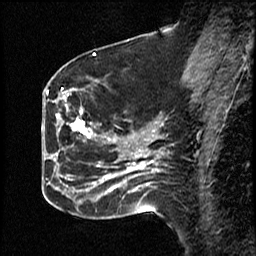
Breast MRI (dynamic contrast-enhanced), one sagittal slice; slice 23 of 50 in the series (ordered by position); dynamic contrast-enhanced study with each time point stored as its own series, time point 2 of 4 at this slice position (early post-contrast, ordered by acquisition time); 1.5 T; TE 4.2 ms, TR 18.5 ms; 256 × 256 image matrix, field of view 200 × 200 mm. Patient: female, 44 years. Case-level facts recorded for this patient, not image findings: setting: breast cancer imaged before/during neoadjuvant chemotherapy; receptor status: HR-positive, HER2-negative.
Annotated regions visible in this slice (semi-automatic segmentation, software-assisted and operator-edited):
- analysis volume of interest (the breast-tissue region the enhancement analysis was run in; not a lesion): box from (x=59, y=89) to (x=114, y=206) px
- tumour enhancement mask (voxels above the 100 % enhancement threshold inside the analysis volume of interest): (x=63, y=97)–(x=114, y=189)